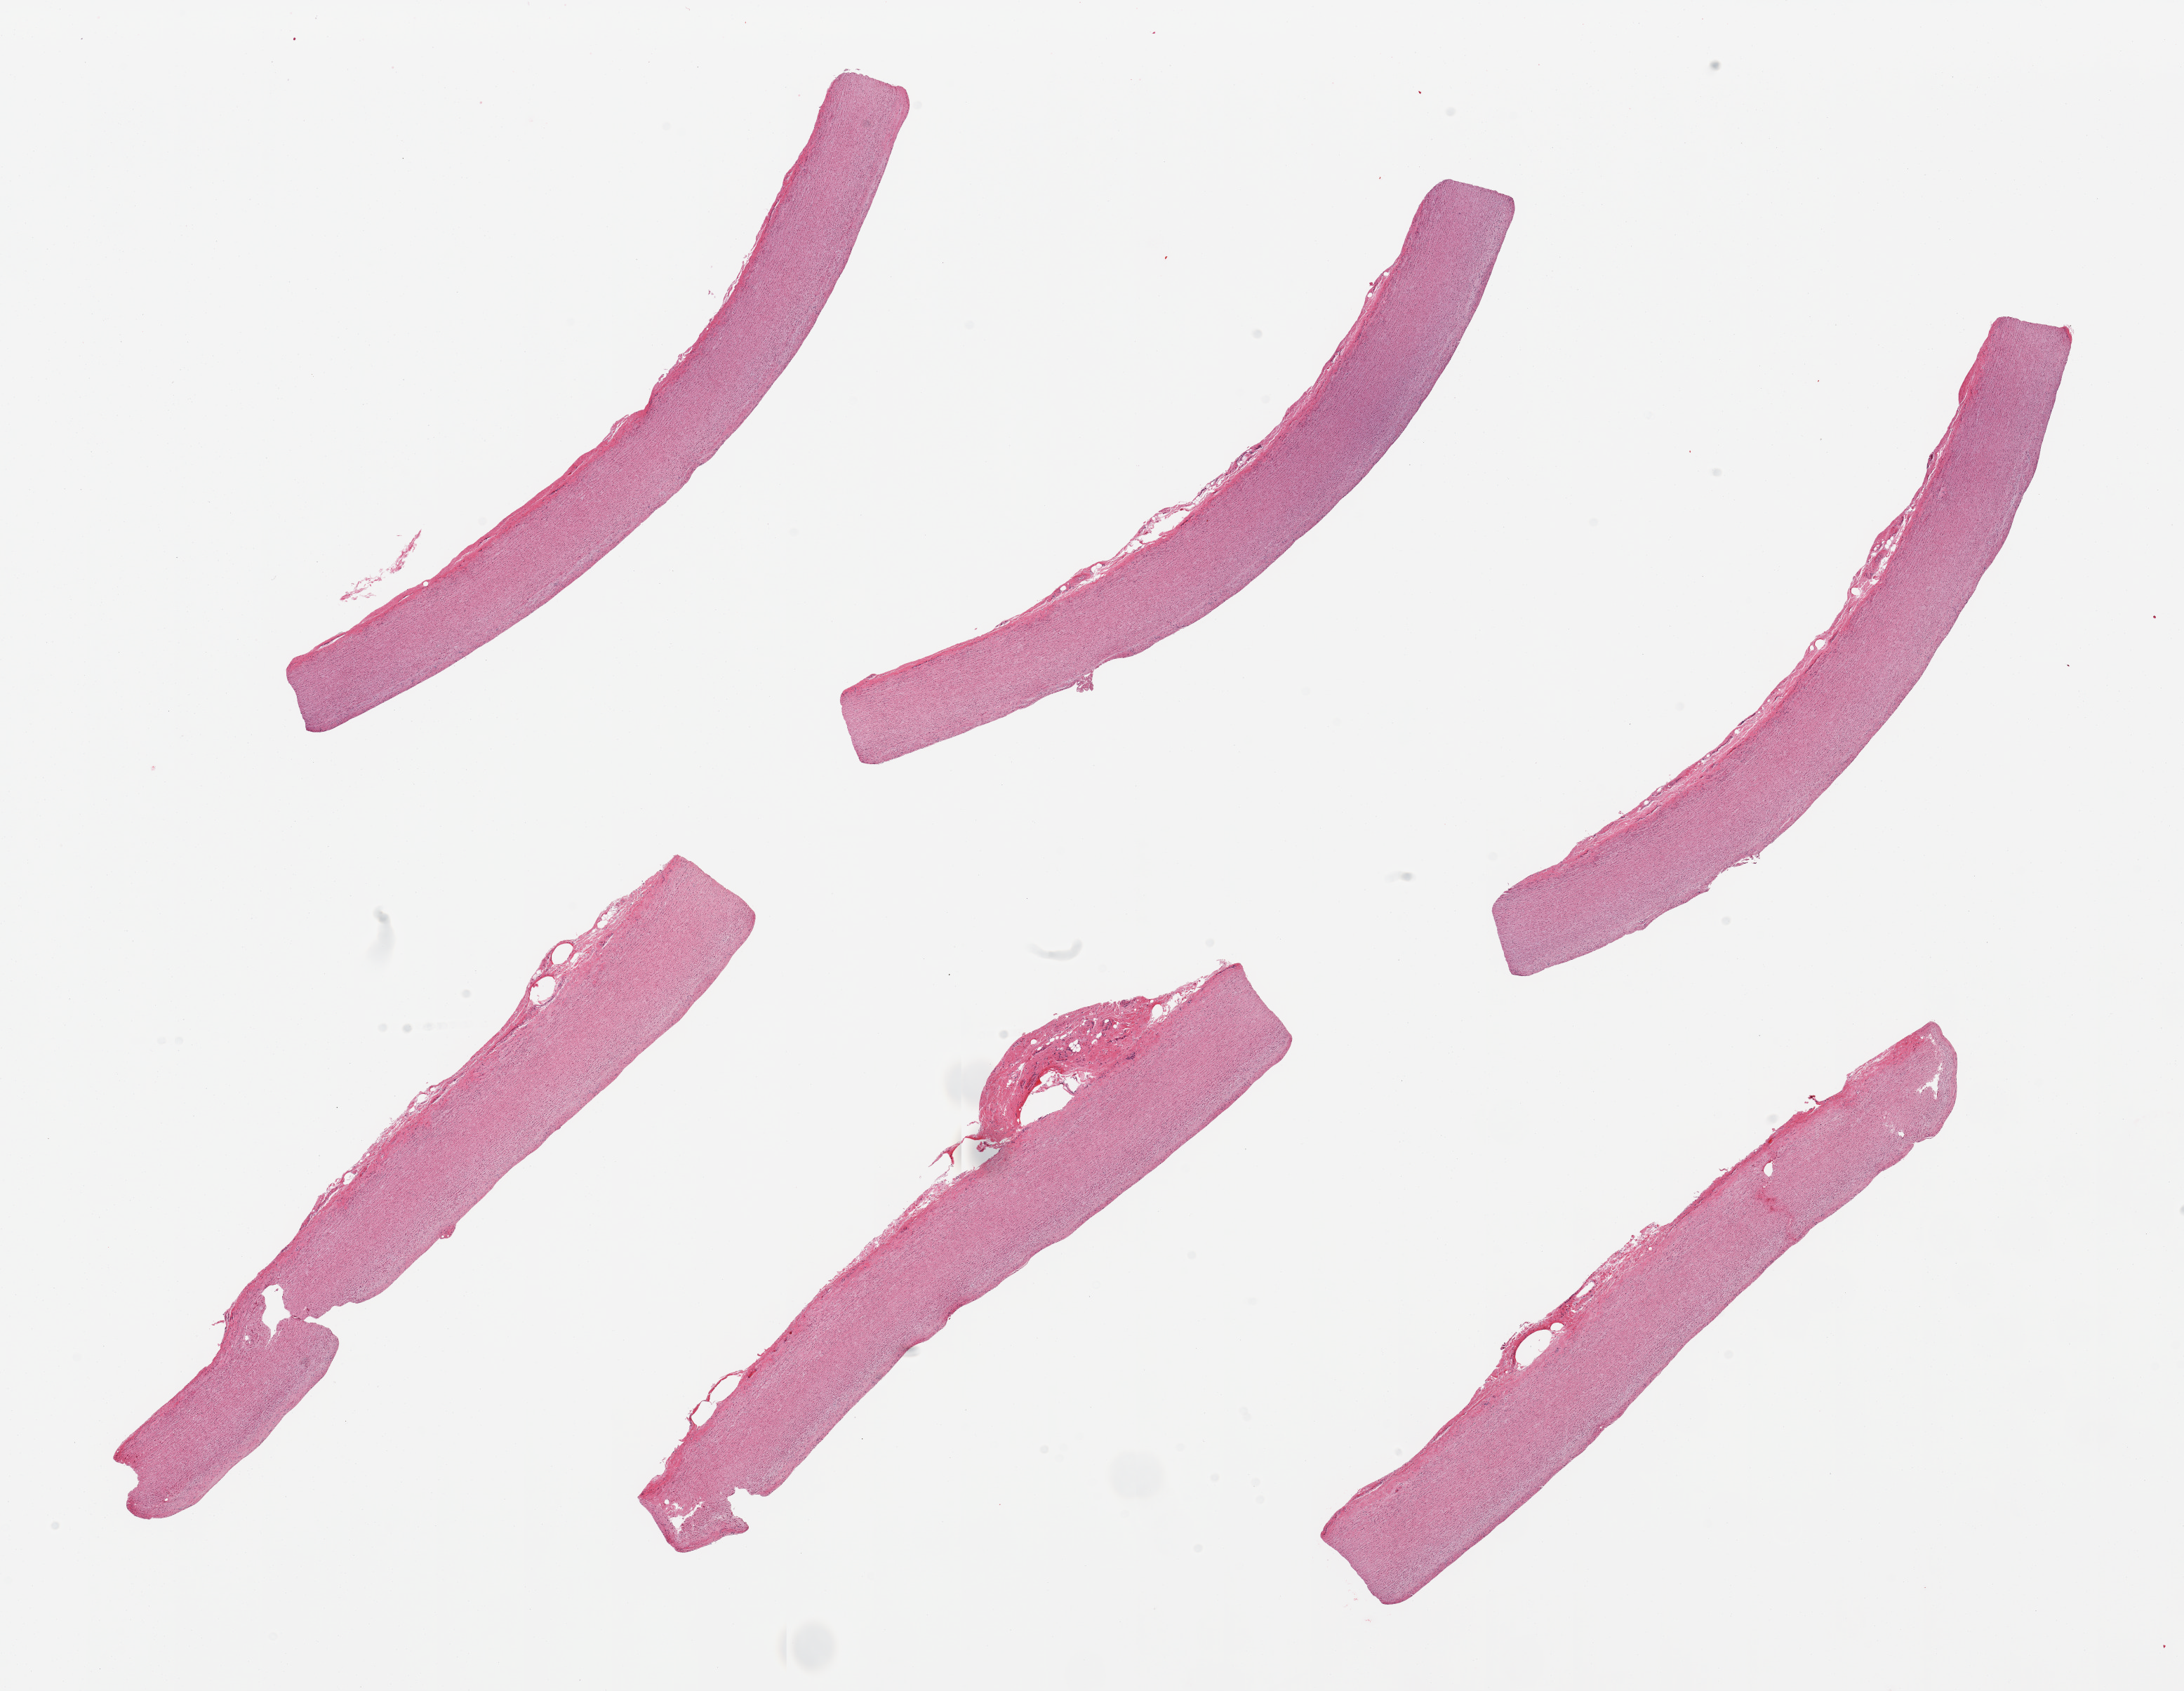
Whole-slide image, haematoxylin and eosin stain, low-resolution overview of the scanned area, about 24.6 x 19.1 mm, PAXgene-fixed paraffin-embedded (PFPE) section, section of aorta (target tissue), donor tissue sample. Donor: male.
Reviewer comment on this tissue sample: 6 pieces.